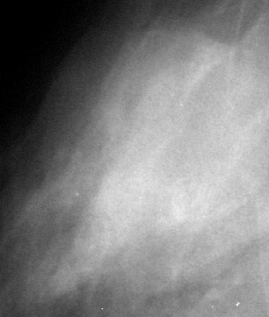
Crop from a digitized film mammogram around one marked abnormality; right breast; CC view.
Finding: mass, shape oval, margins circumscribed / ill defined; BI-RADS assessment category 4; subtlety rating 4 on a 1 (subtle) to 5 (obvious) scale; pathology (as recorded): benign.